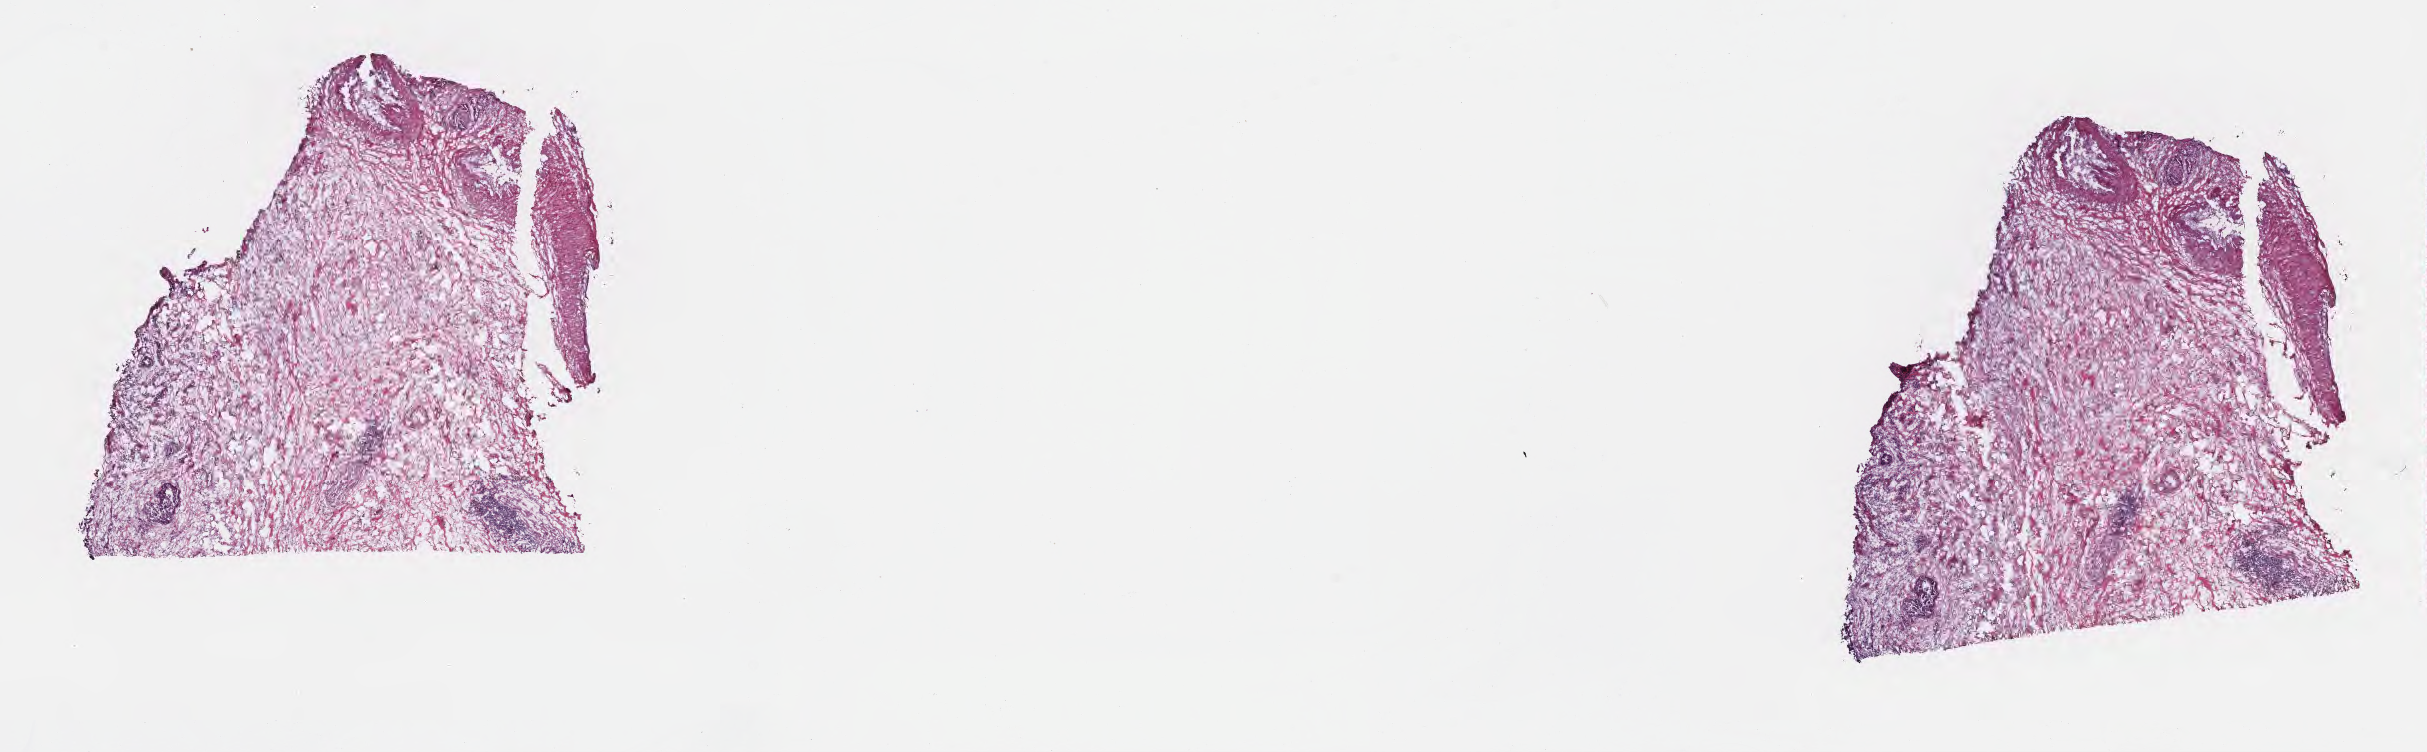
Haematoxylin and eosin whole-slide image, whole scanned area (about 19.6 x 6.1 mm) shown as a low-resolution overview, cryosection, specimen: primary tumor, site: head of pancreas. Female patient; age at initial diagnosis 73 years. Tumor grade: G2 (moderately differentiated). Slide review estimates, as recorded: tumor cells 10%, tumor nuclei 80%, stromal cells 90%, necrosis 0%, normal cells 0%. Inflammatory infiltration, as recorded: lymphocyte infiltration 0%, monocyte infiltration 0%, neutrophil infiltration 0%.
Histologic diagnosis: Infiltrating duct carcinoma, NOS. AJCC pathologic stage: Stage III.